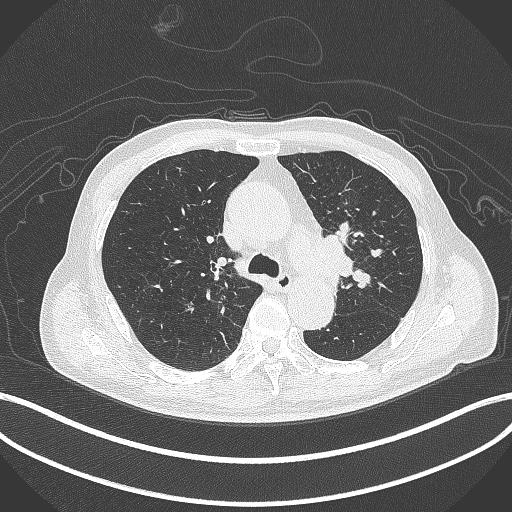
Chest CT, one axial slice; position 295 of 417 along the scan axis; reconstruction kernel B70f; lung window (W 1500 / L -600 HU); 512 × 512 image matrix, field of view 400 × 400 mm. Patient: male, 77 years. Case-level facts recorded for this patient, not image findings: clinical TNM (as recorded): T3 N1 M0.
Annotated regions visible in this slice (rectangle marked by the reading radiologist):
- lung tumour (recorded histology: adenocarcinoma): bounding box [x1, y1, x2, y2] px = [316, 227, 358, 282]